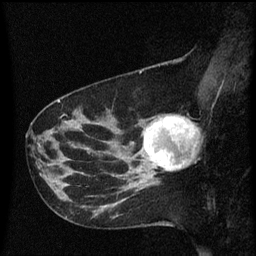
Breast MRI (dynamic contrast-enhanced), one sagittal slice; position 22 of 60 along the scan axis; dynamic contrast-enhanced series, image 2 of 3 at this slice position (ordered by acquisition); 1.5 T; TE 4.2 ms, TR 8.4 ms; 2 mm slice thickness; 256 × 256 image matrix. Female patient, age 41 years. From the clinical record (not read from this slice): setting: breast cancer imaged before/during neoadjuvant chemotherapy; receptor status: triple-negative.
Annotated regions visible in this slice (semi-automatically segmented with operator editing):
- analysis volume of interest (the breast-tissue region the enhancement analysis was run in; not a lesion): bounding box (x1, y1, x2, y2) in pixels: (138, 114, 196, 177)
- tumour enhancement mask (voxels above the 70 % enhancement threshold inside the analysis volume of interest): (143, 118, 195, 171)